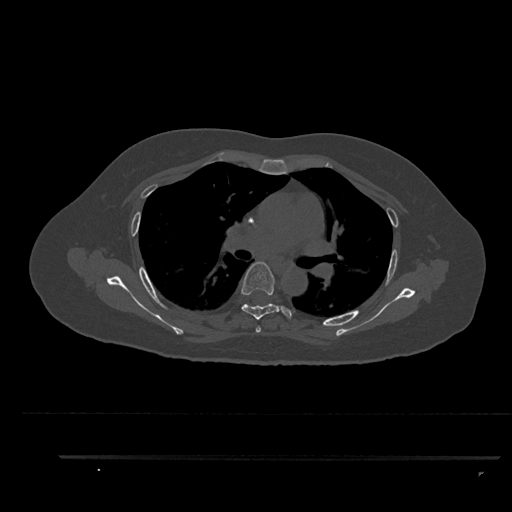
CT including the spine, one axial slice; slice 601 of 797 in the series (ordered by position); bone window (W 1800 / L 400 HU); 0.5 mm slice thickness; 512 × 512 image matrix, field of view 408 × 408 mm. Patient: female, 44 years. Case-level facts recorded for this patient, not image findings: primary cancer: renal.
Outlined on this slice (semi-automatically segmented with operator editing):
- T4 vertebra: bounding box (x1, y1, x2, y2) in pixels: (256, 326, 261, 333)
- T5 vertebra: (241, 262, 292, 320)
- T6 vertebra: (262, 304, 269, 307)